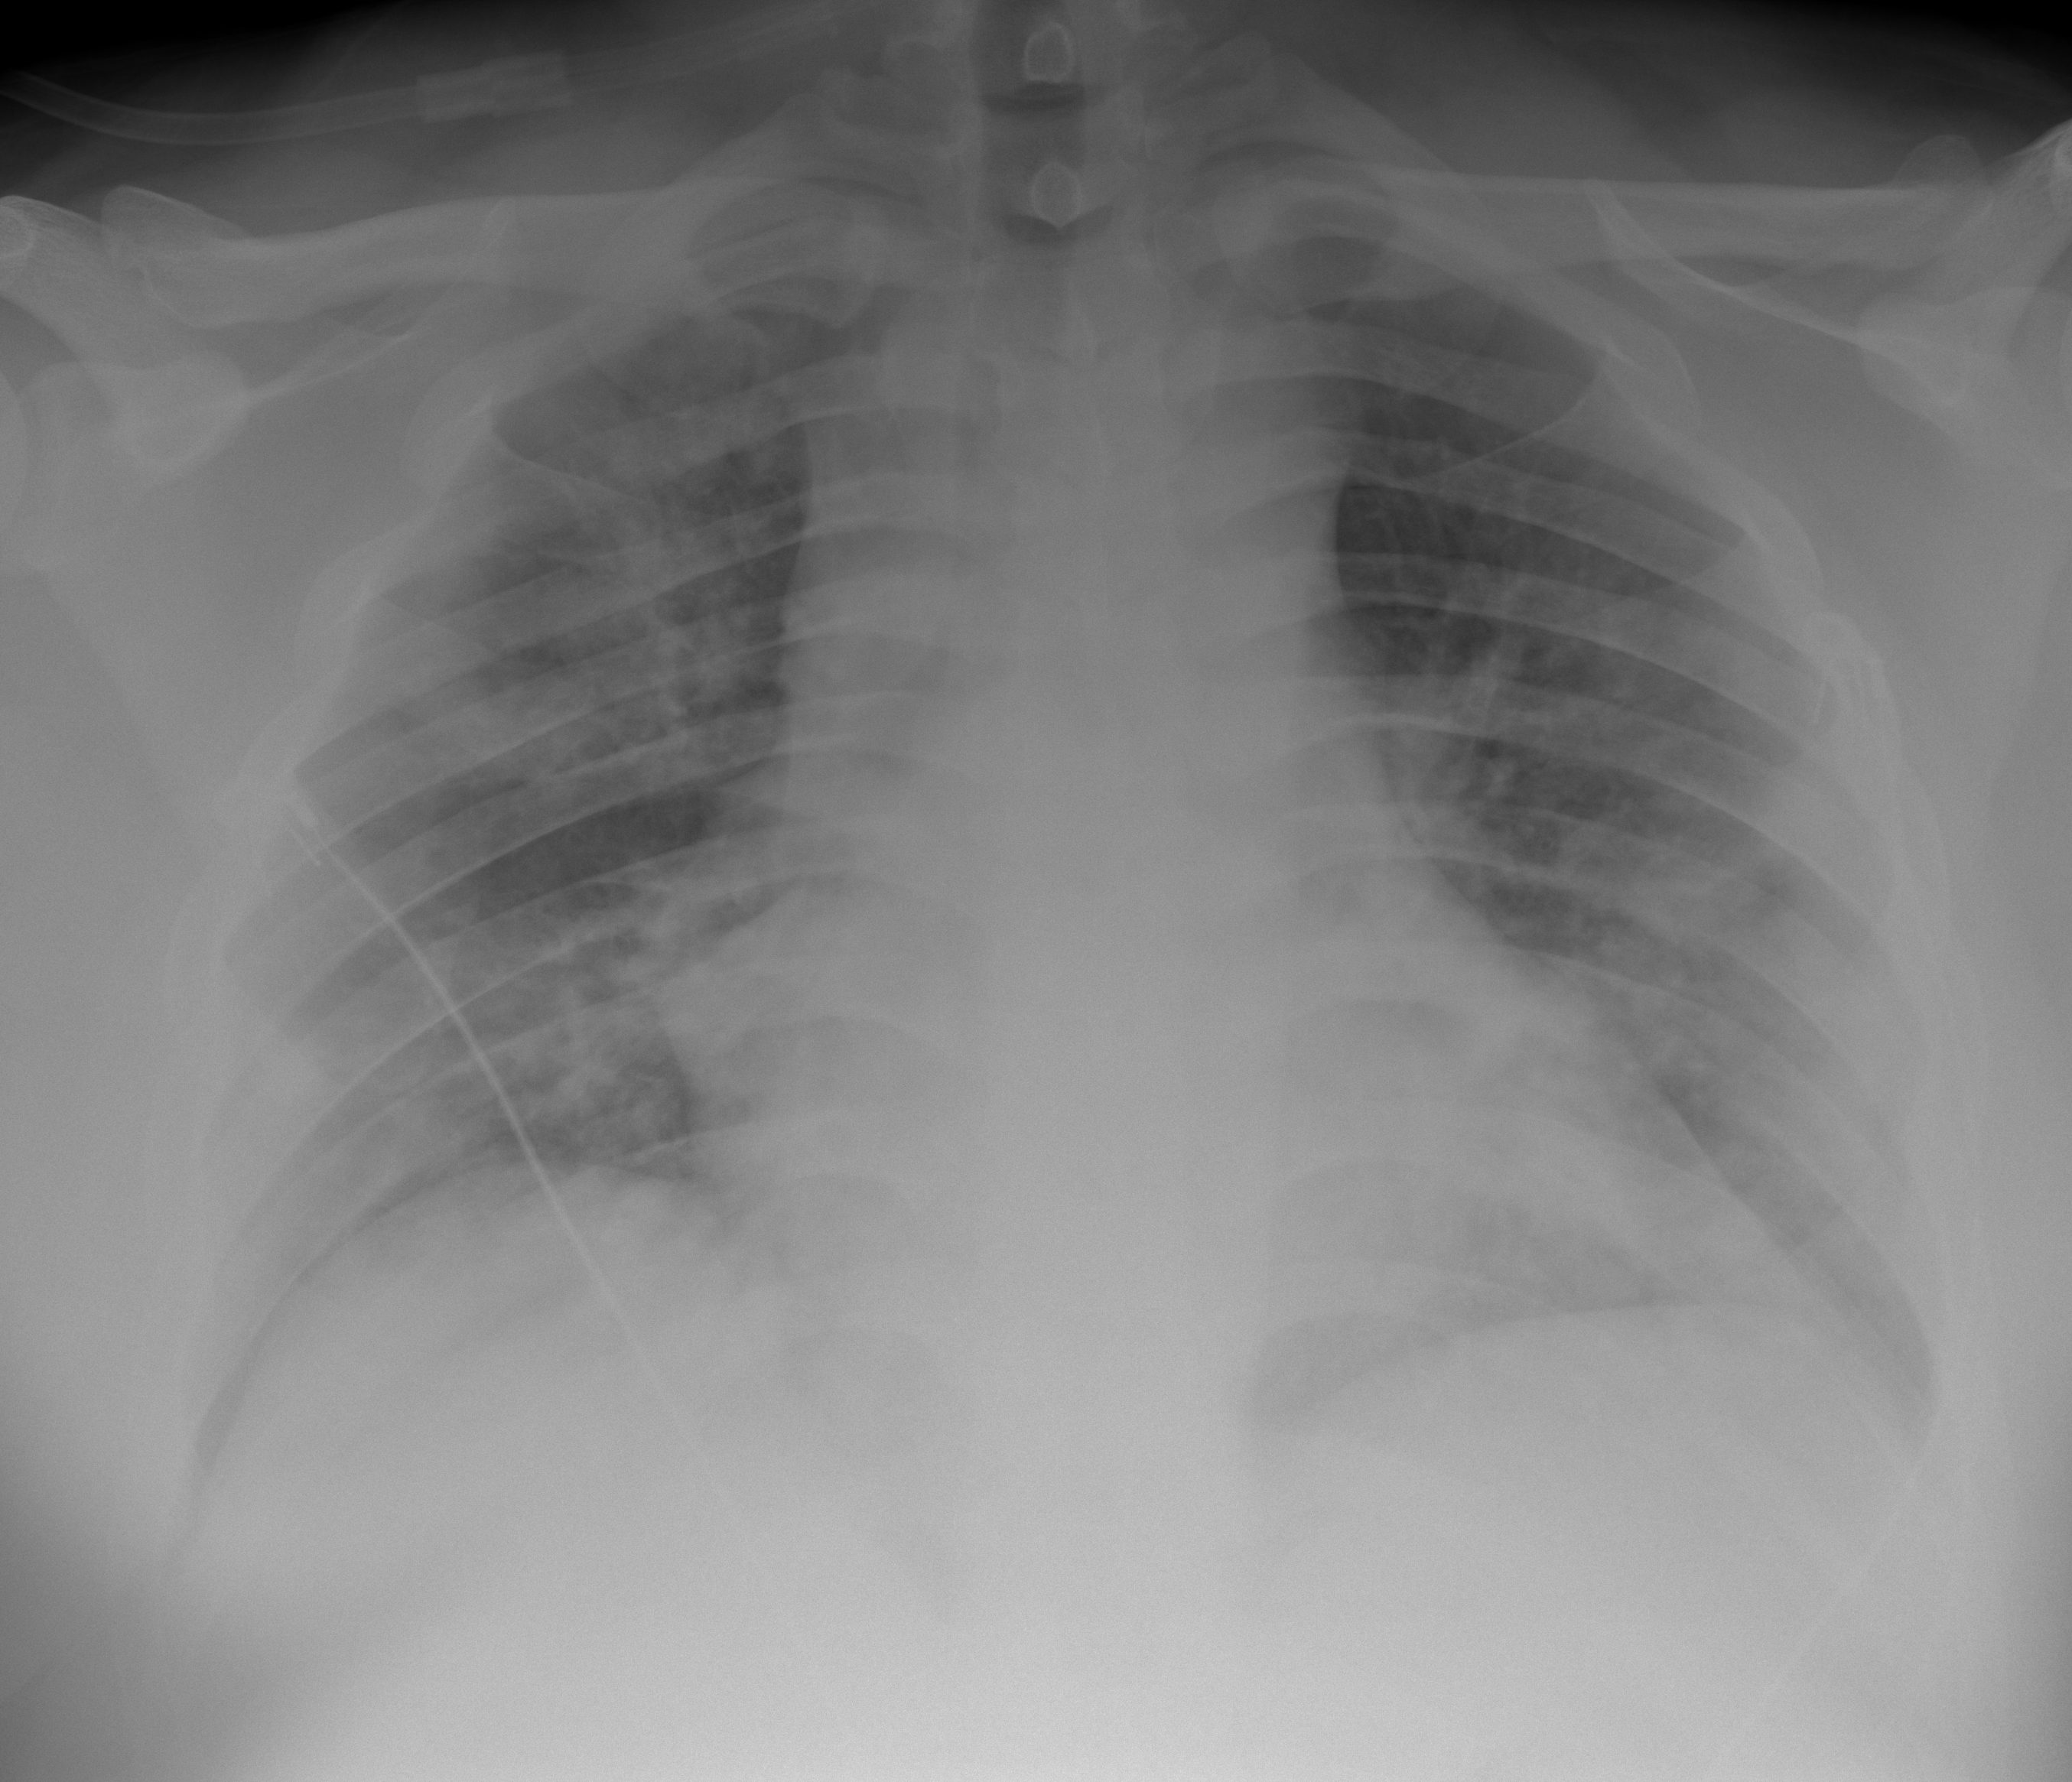
Portable chest radiograph, AP projection. Male patient, age 25 years; imaged 0 days after the COVID-19 diagnosis.
Key findings recorded by the radiologist: subtle hazy opacity and left lower lobe consistent with ground-glass airspace disease, minimal right infrahilar airspace opacity, slight hazy right perihilar opacity.